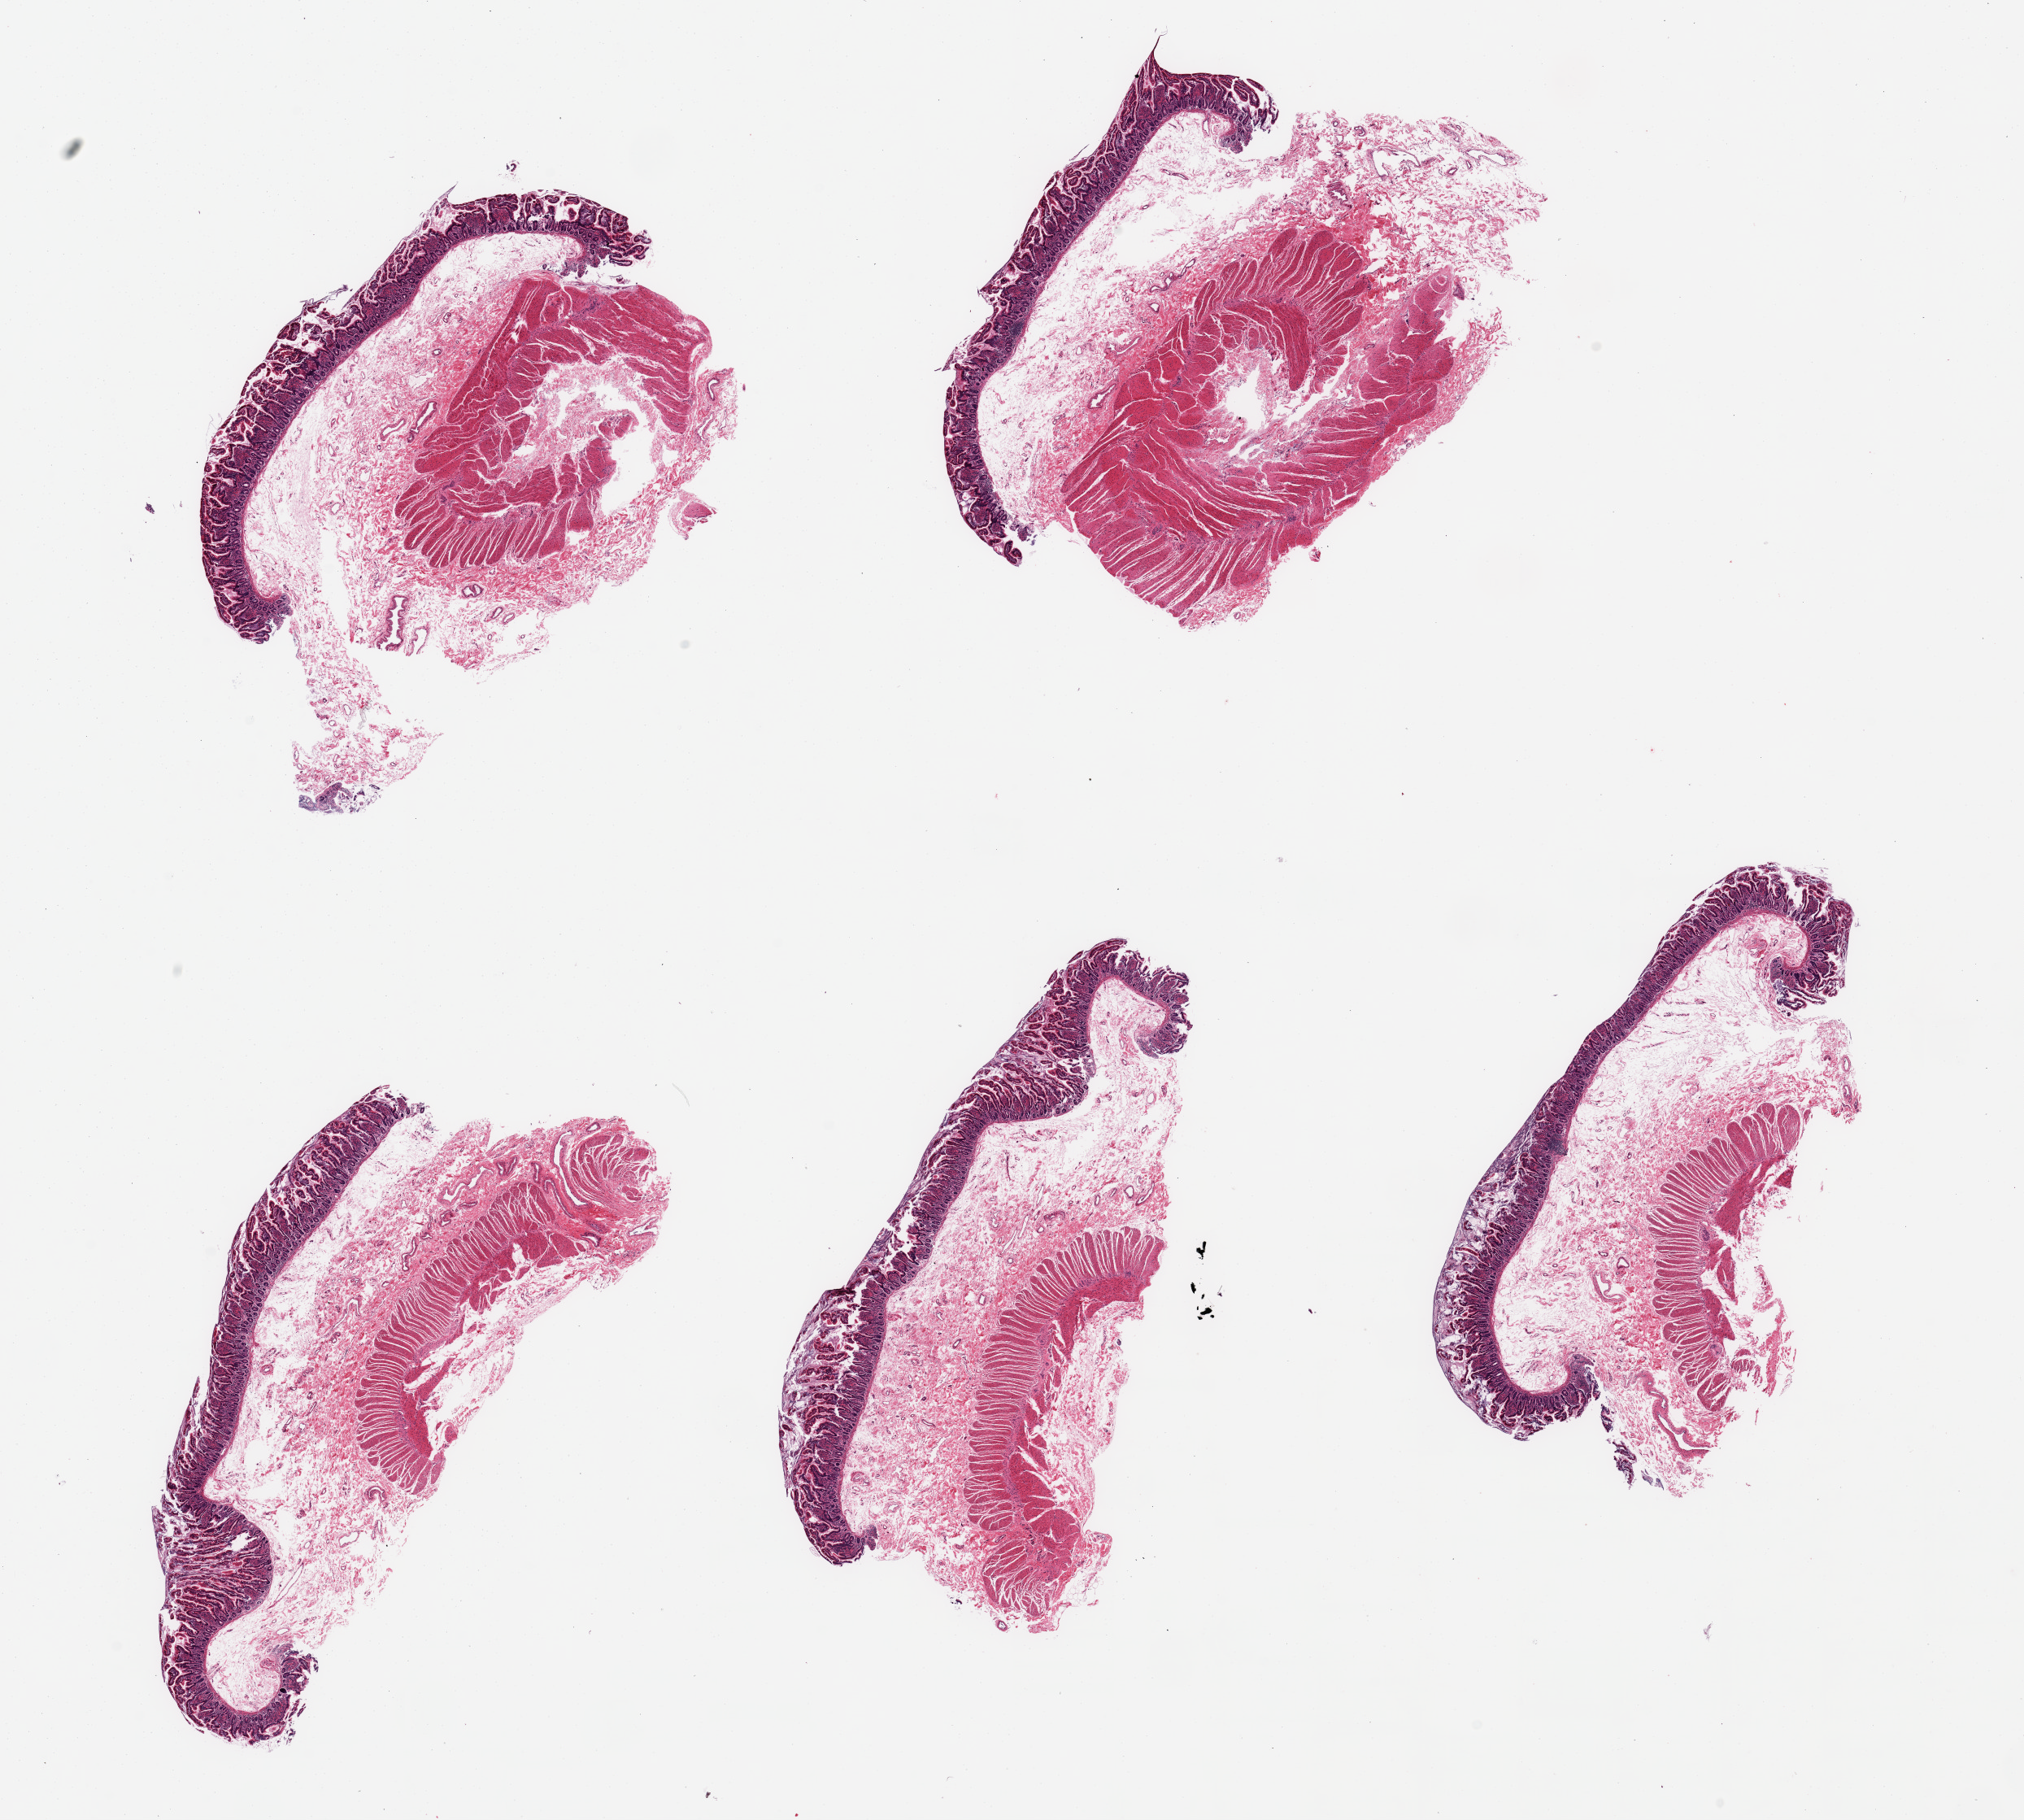
Whole-slide image, haematoxylin and eosin stain, a low-resolution overview of the entire scanned area, about 19.7 x 17.7 mm (acquisition: 20x scan). PAXgene-fixed paraffin-embedded (PFPE) section. Sampled site (target tissue): sigmoid colon. Tissue donor sample.
Pathologist's review note for this sample: 5 pieces, sections of small bowel, not sigmoid muscularis.